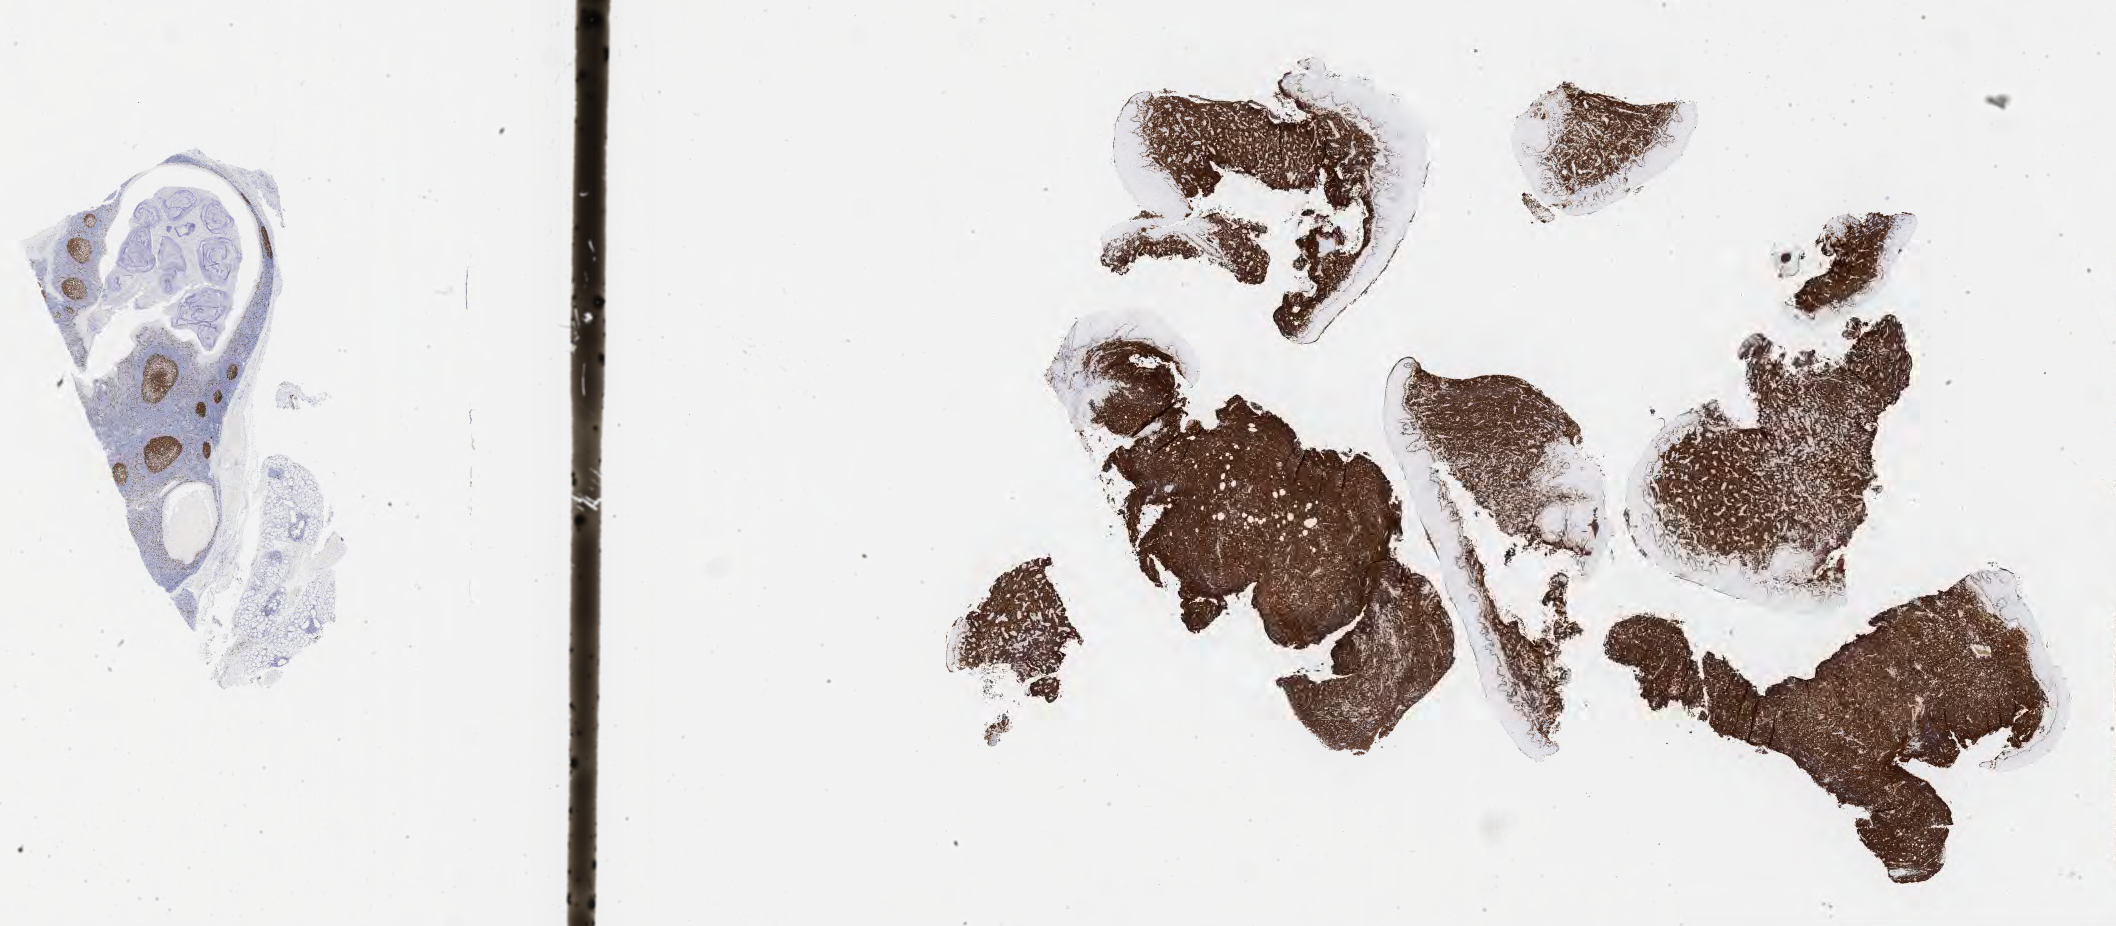
Immunohistochemistry (IHC) whole-slide image stained for Ki-67 — shown as a low-resolution overview of the whole scanned area (about 34.2 x 15.0 mm). Tumor tissue. Male patient, aged 43.
Diagnosis: Burkitt lymphoma, NOS.